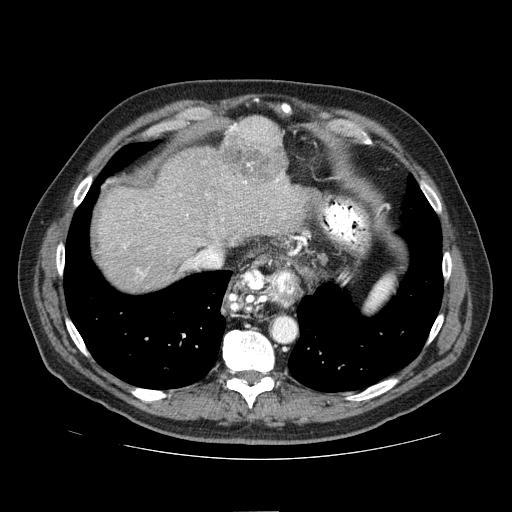
Contrast-enhanced abdominal CT (liver protocol), one axial slice. Position 63 of 81 along the scan axis. Reconstruction kernel STANDARD. 100 kVp. One of 2 acquisitions stored at this slice position. Soft-tissue window (W 400 / L 40 HU). 512 × 512 image matrix, field of view 400 × 400 mm. From the clinical record (not read from this slice): diagnosis: hepatocellular carcinoma (patient treated with transarterial chemoembolisation; whether this scan precedes or follows treatment is not stated here); TNM stage (as recorded): Stage-IIIA; Child-Pugh class: A; tumour size: 5.6 cm.
Annotated regions visible in this slice (semi-automatic segmentation, software-assisted and operator-edited):
- abdominal aorta: bounding box [x1, y1, x2, y2] px = [273, 318, 295, 341]
- liver parenchyma outside the tumour (the mass and vessels are separate outlines, so this box may not span the whole liver): [96, 118, 308, 290]
- mass: [218, 116, 286, 184]
- liver vessels: [123, 180, 287, 277]